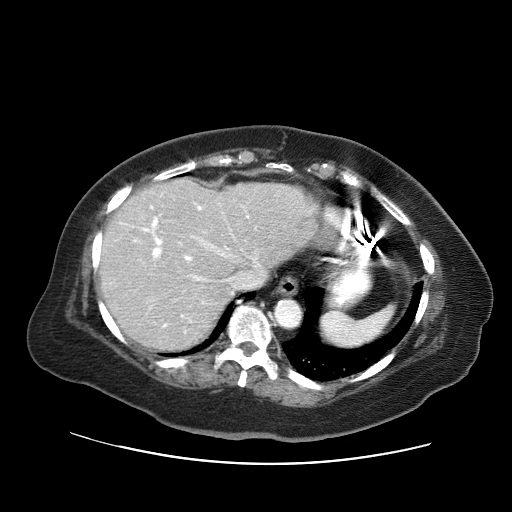
Contrast-enhanced abdominal CT (liver protocol), one axial slice. Position 48 of 71 along the scan axis. Reconstruction kernel STANDARD. 120 kVp. Soft-tissue window (W 400 / L 40 HU). 2.5 mm slice thickness. 512 × 512 image matrix, field of view 400 × 400 mm. Case-level facts recorded for this patient, not image findings: diagnosis: hepatocellular carcinoma (patient treated with transarterial chemoembolisation; whether this scan precedes or follows treatment is not stated here); TNM stage (as recorded): Stage-II; Child-Pugh class: A; tumour differentiation: poorly differentiated.
Annotated regions visible in this slice (semi-automatically segmented with operator editing):
- liver parenchyma outside the tumour (the mass and vessels are separate outlines, so this box may not span the whole liver): bounding box (x1, y1, x2, y2) in pixels: (98, 178, 318, 350)
- liver vessels: (120, 203, 261, 333)